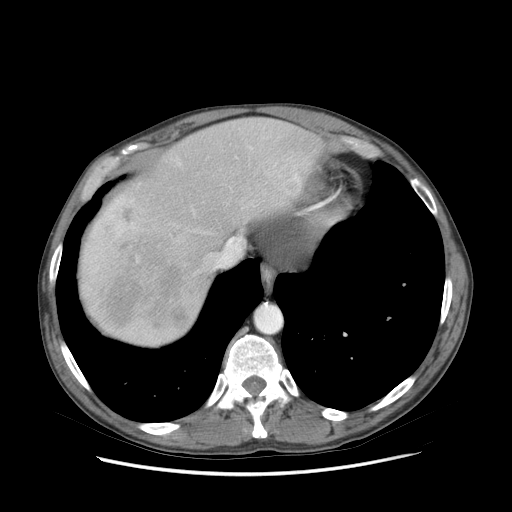
Contrast-enhanced abdominal CT (liver protocol), one axial slice; position 68 of 89 along the scan axis; 140 kVp; soft-tissue window (W 400 / L 40 HU); 2.5 mm slice thickness; 512 × 512 image matrix, field of view 380 × 380 mm. From the clinical record (not read from this slice): diagnosis: hepatocellular carcinoma (patient treated with transarterial chemoembolisation; whether this scan precedes or follows treatment is not stated here); TNM stage (as recorded): Stage-IIIB; Child-Pugh class: A; tumour differentiation: moderately differentiated.
Outlined on this slice (semi-automatically segmented with operator editing):
- abdominal aorta: bounding box (x1, y1, x2, y2) in pixels: (257, 306, 280, 332)
- liver parenchyma outside the tumour (the mass and vessels are separate outlines, so this box may not span the whole liver): (80, 118, 324, 346)
- mass: (95, 241, 189, 328)
- liver vessels: (91, 146, 300, 272)